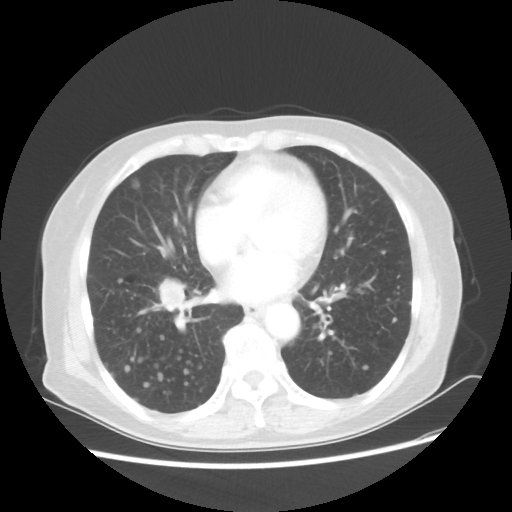
Chest CT, one axial slice; position 23 of 56 along the scan axis; reconstruction kernel STANDARD; 80 kVp; lung window (W 1500 / L -600 HU); 5 mm slice thickness; 512 × 512 image matrix. Female patient, age 68 years. From the clinical record (not read from this slice): clinical TNM (as recorded): T1c N3 M0.
Outlined on this slice (rectangle marked by the reading radiologist):
- lung tumour (recorded histology: squamous cell carcinoma): bounding box [x1, y1, x2, y2] px = [145, 270, 195, 323]